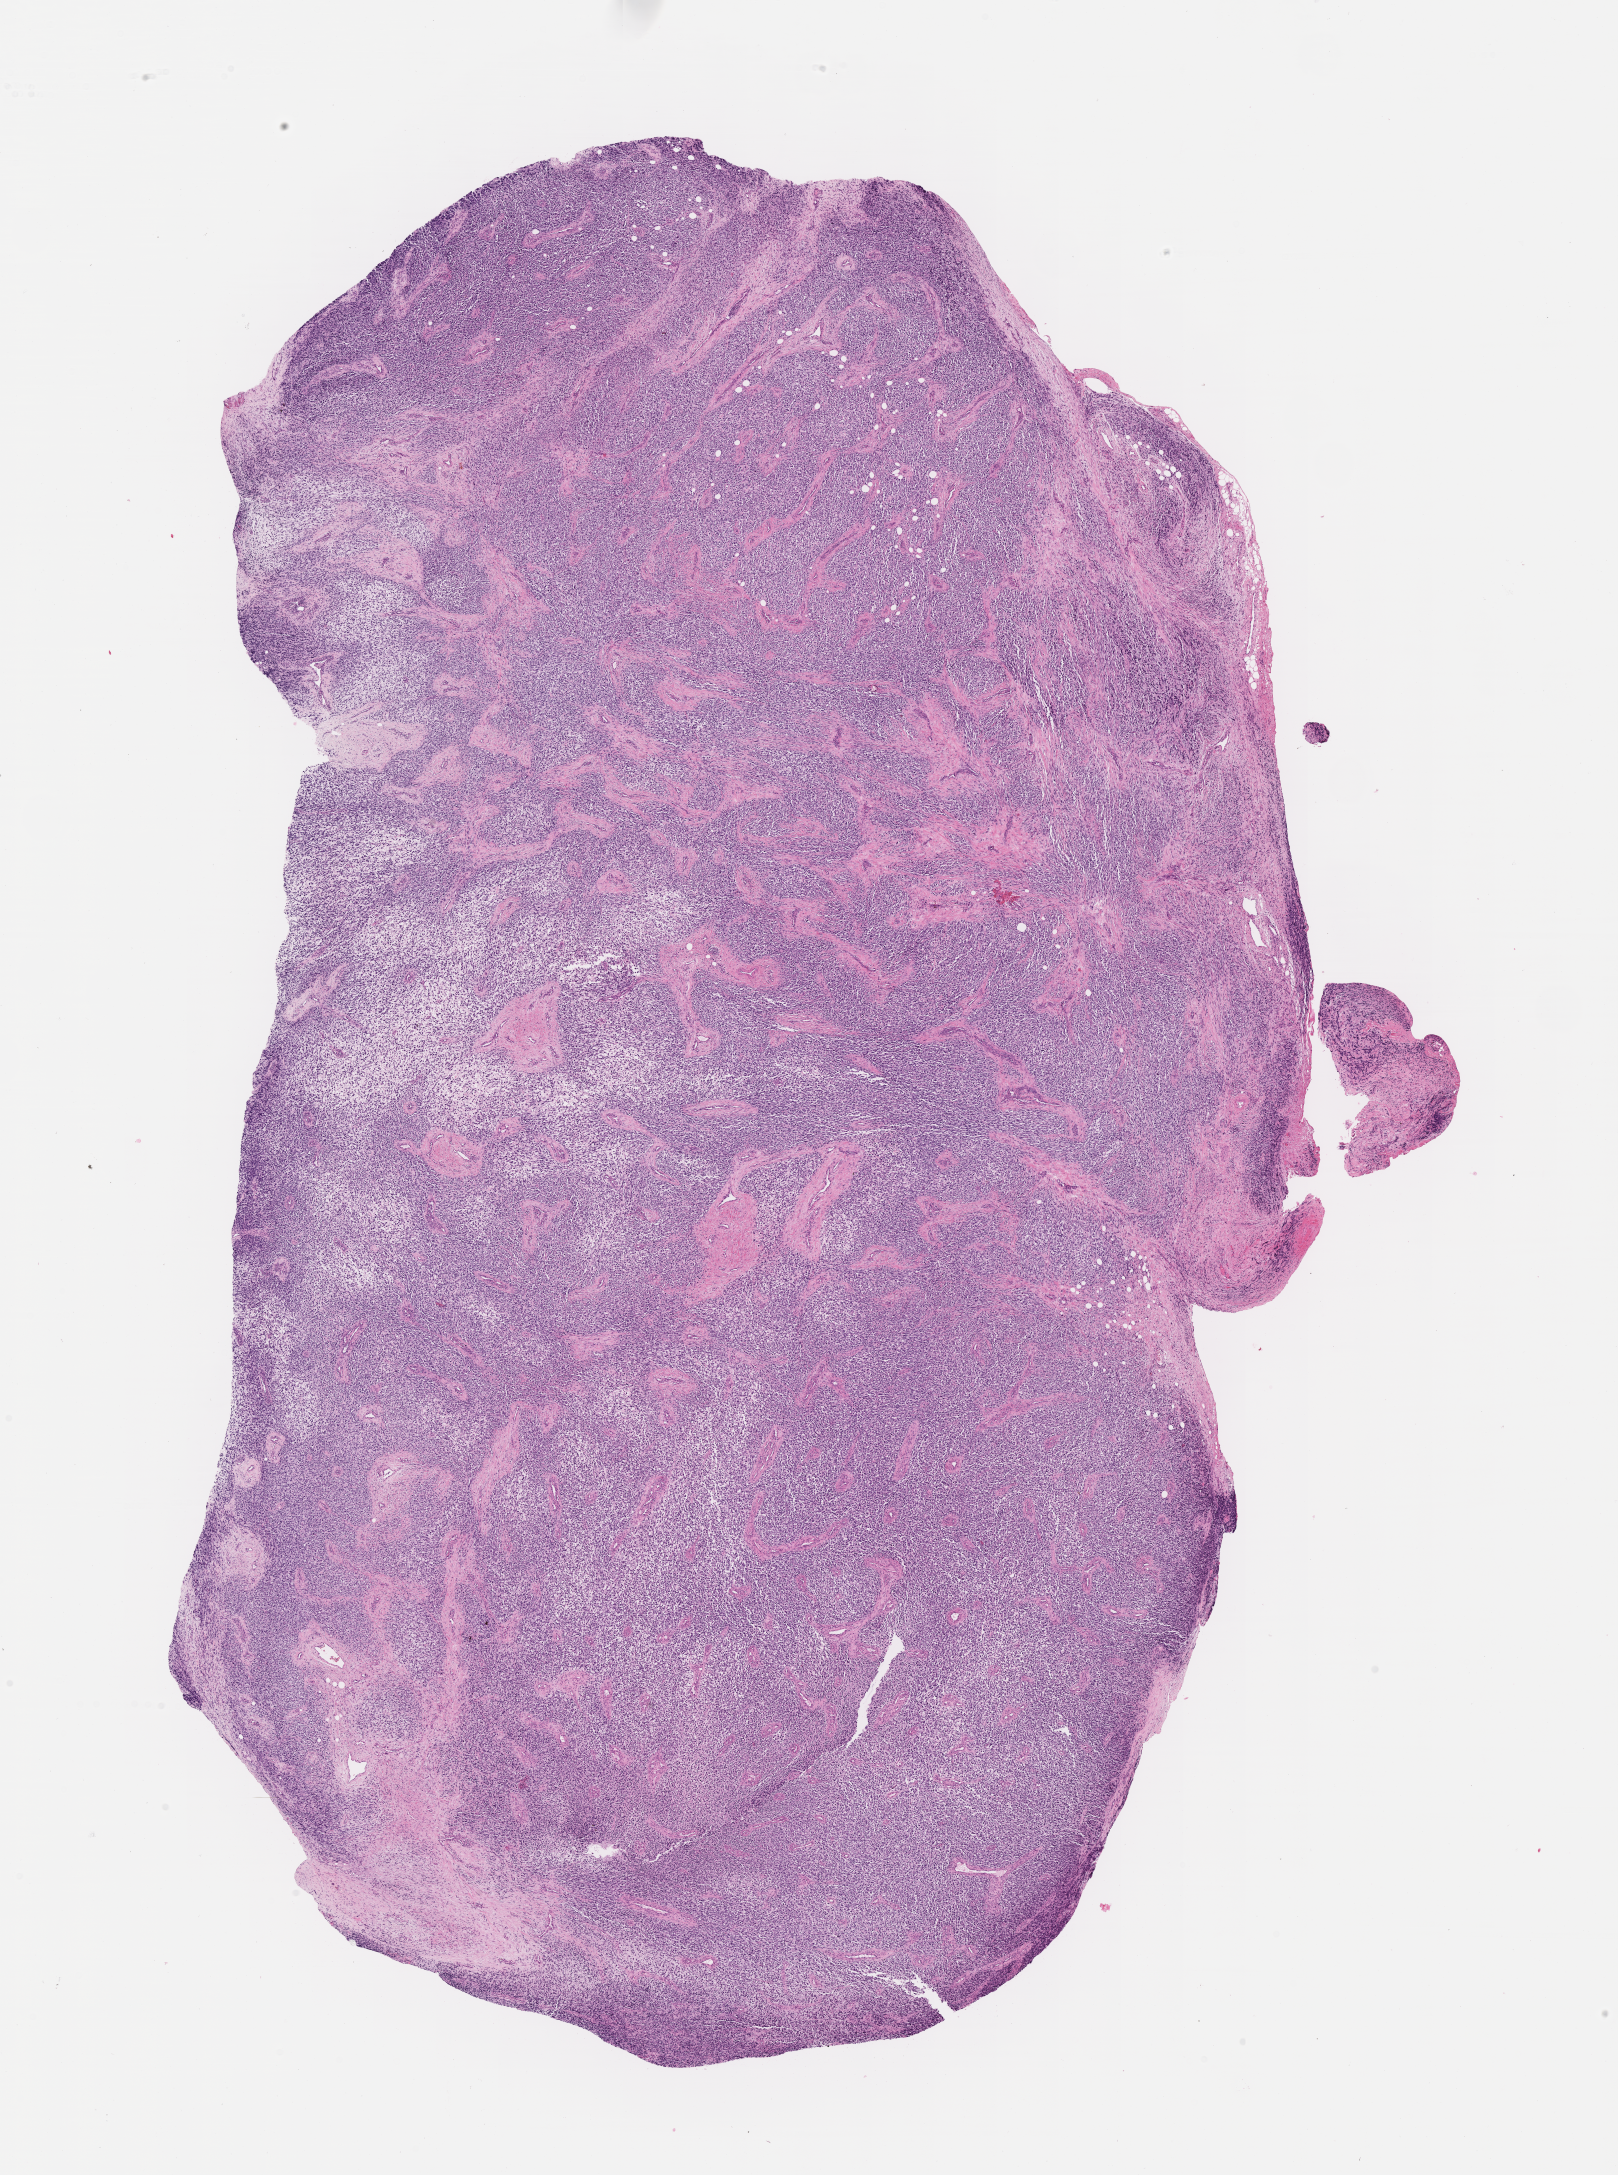
Whole-slide image, haematoxylin and eosin stain of tumor tissue — whole scanned area (about 13.1 x 17.6 mm) shown as a low-resolution overview; FFPE section; sample anatomic site: orbit, left anterior. Male patient, age at diagnosis 6.2 years.
* stage (as recorded): 1
* diagnosis: rhabdomyosarcoma; histological classification: embryonal rhabdomyosarcoma
* metastatic status at presentation (as recorded): non-metastatic (confirmed)